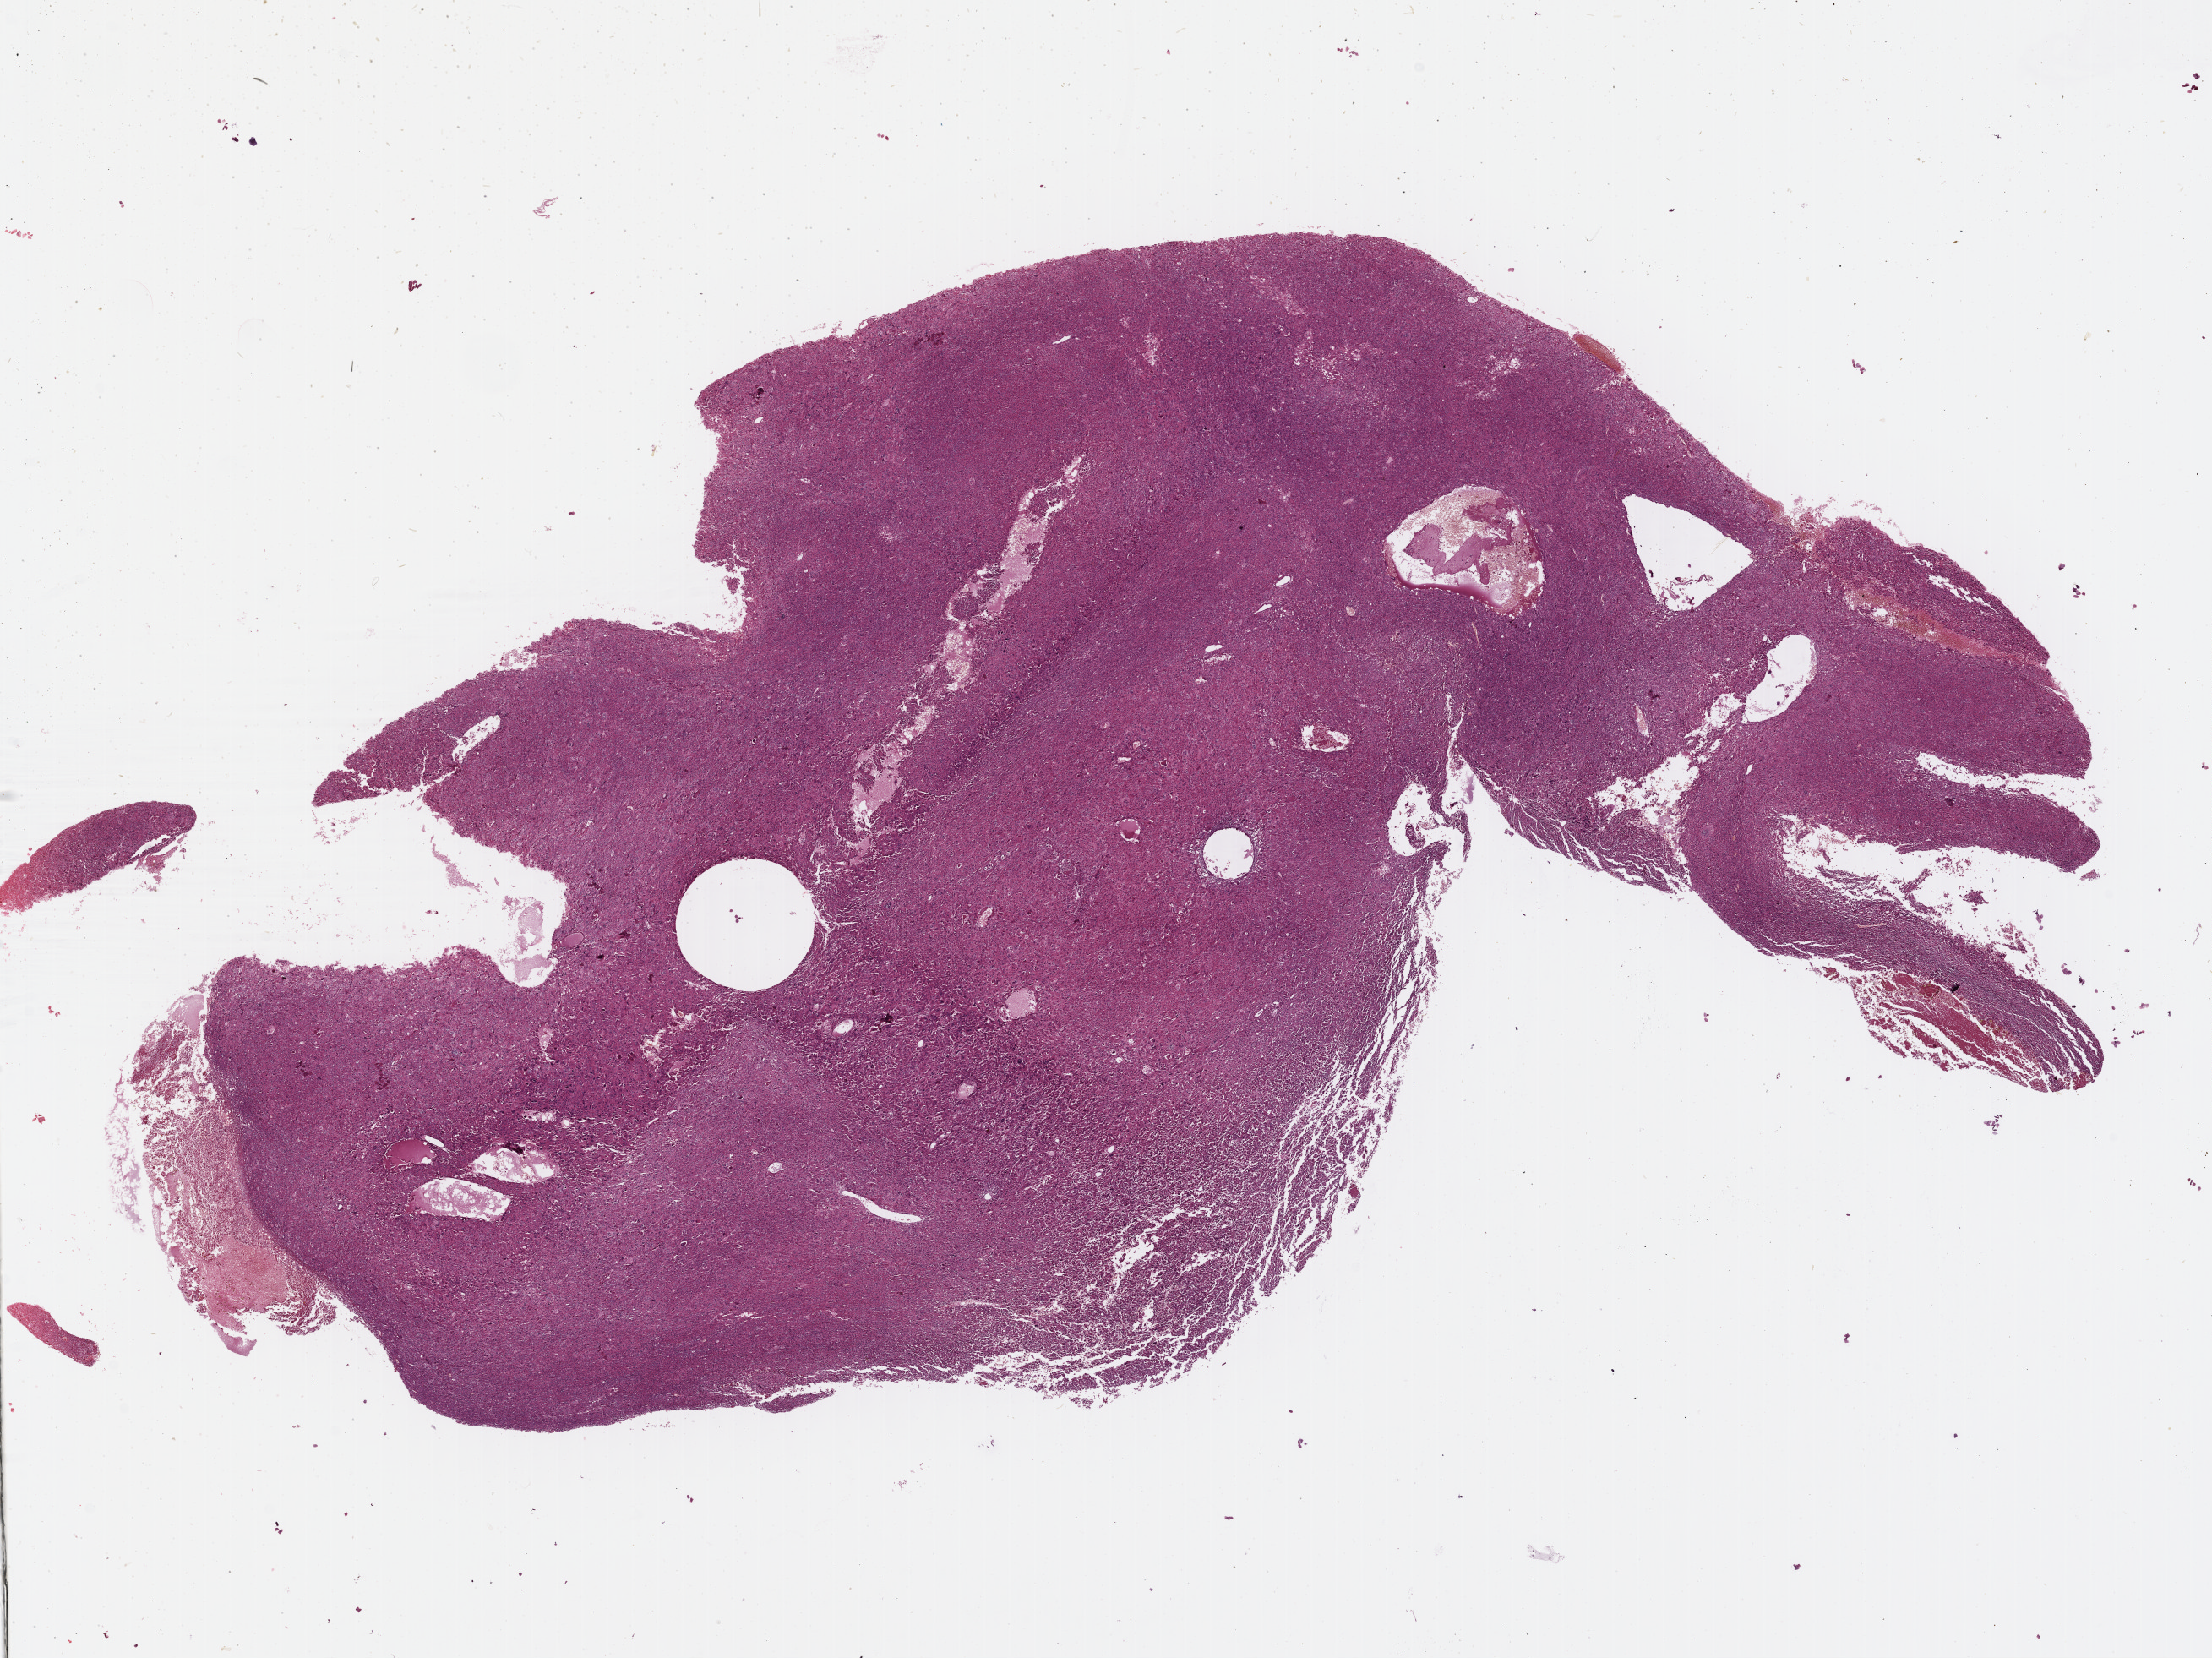
Digitized H&E-stained tissue section (whole slide) — low-resolution overview of the scanned area, about 20.6 x 15.4 mm (acquisition: 40x scan), FFPE section, sample: primary tumour, liver. Male patient; age at initial diagnosis 45 years. Histologic grade: G2 (moderately differentiated).
• pathologic diagnosis: Hepatocellular carcinoma, NOS
• AJCC pathologic stage: IIIA (6th edition)